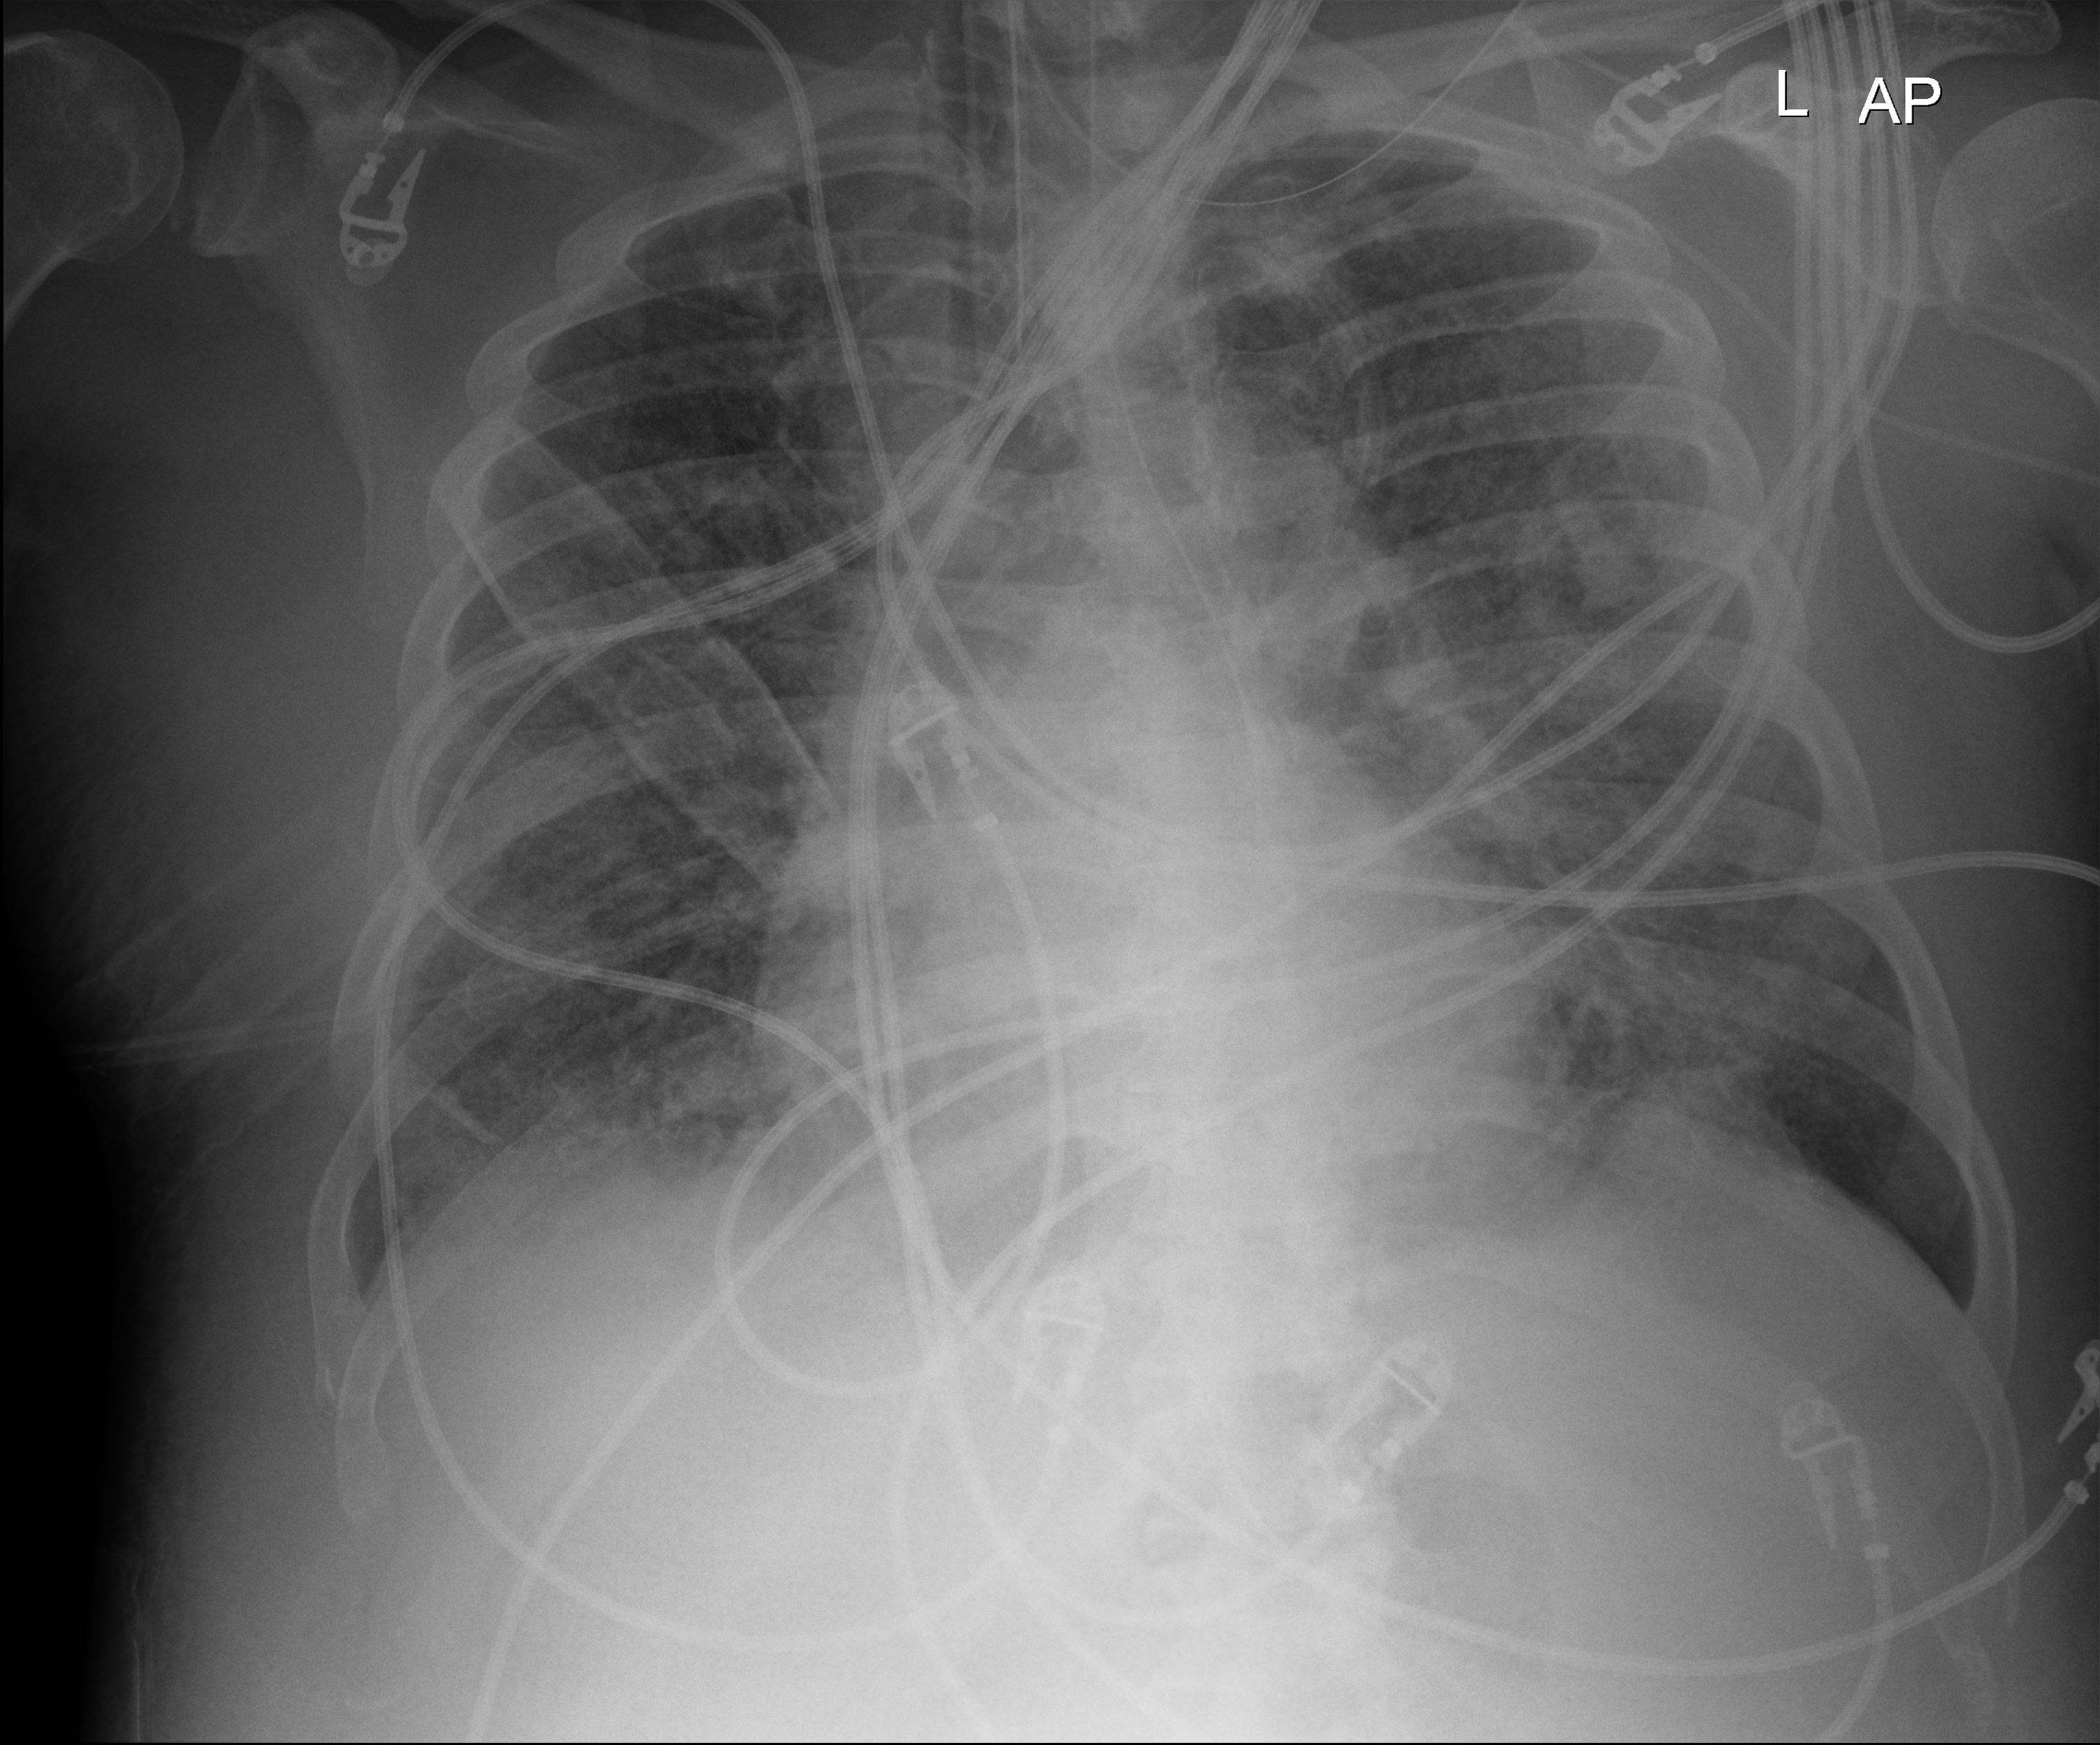
Chest X-ray (portable), anteroposterior (AP) projection. Male patient hospitalised with COVID-19, age 60–74 years.
Admission-level facts for this patient (not findings on this image; timing relative to this image not recorded):
- other chronic lung disease (admission record): no
- mechanically ventilated during this hospital stay: yes
- admitted to intensive care during this hospital stay: yes